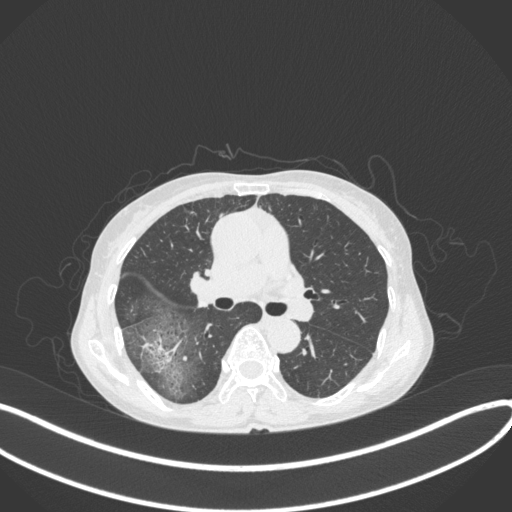
Chest CT, one axial slice. Slice 235 of 379 in the series (ordered by position). Reconstruction kernel B31f. 120 kVp. Lung window (W 1500 / L -600 HU). 1 mm slice thickness. 512 × 512 image matrix, field of view 400 × 400 mm. Patient: female, 69 years. From the clinical record (not read from this slice): clinical TNM (as recorded): T1b N0 M0; histopathological grade: G2-3.
Structures marked on this image (bounding box drawn by a radiologist):
- lung tumour (recorded histology: adenocarcinoma): bounding box [x1, y1, x2, y2] px = [141, 332, 186, 376]